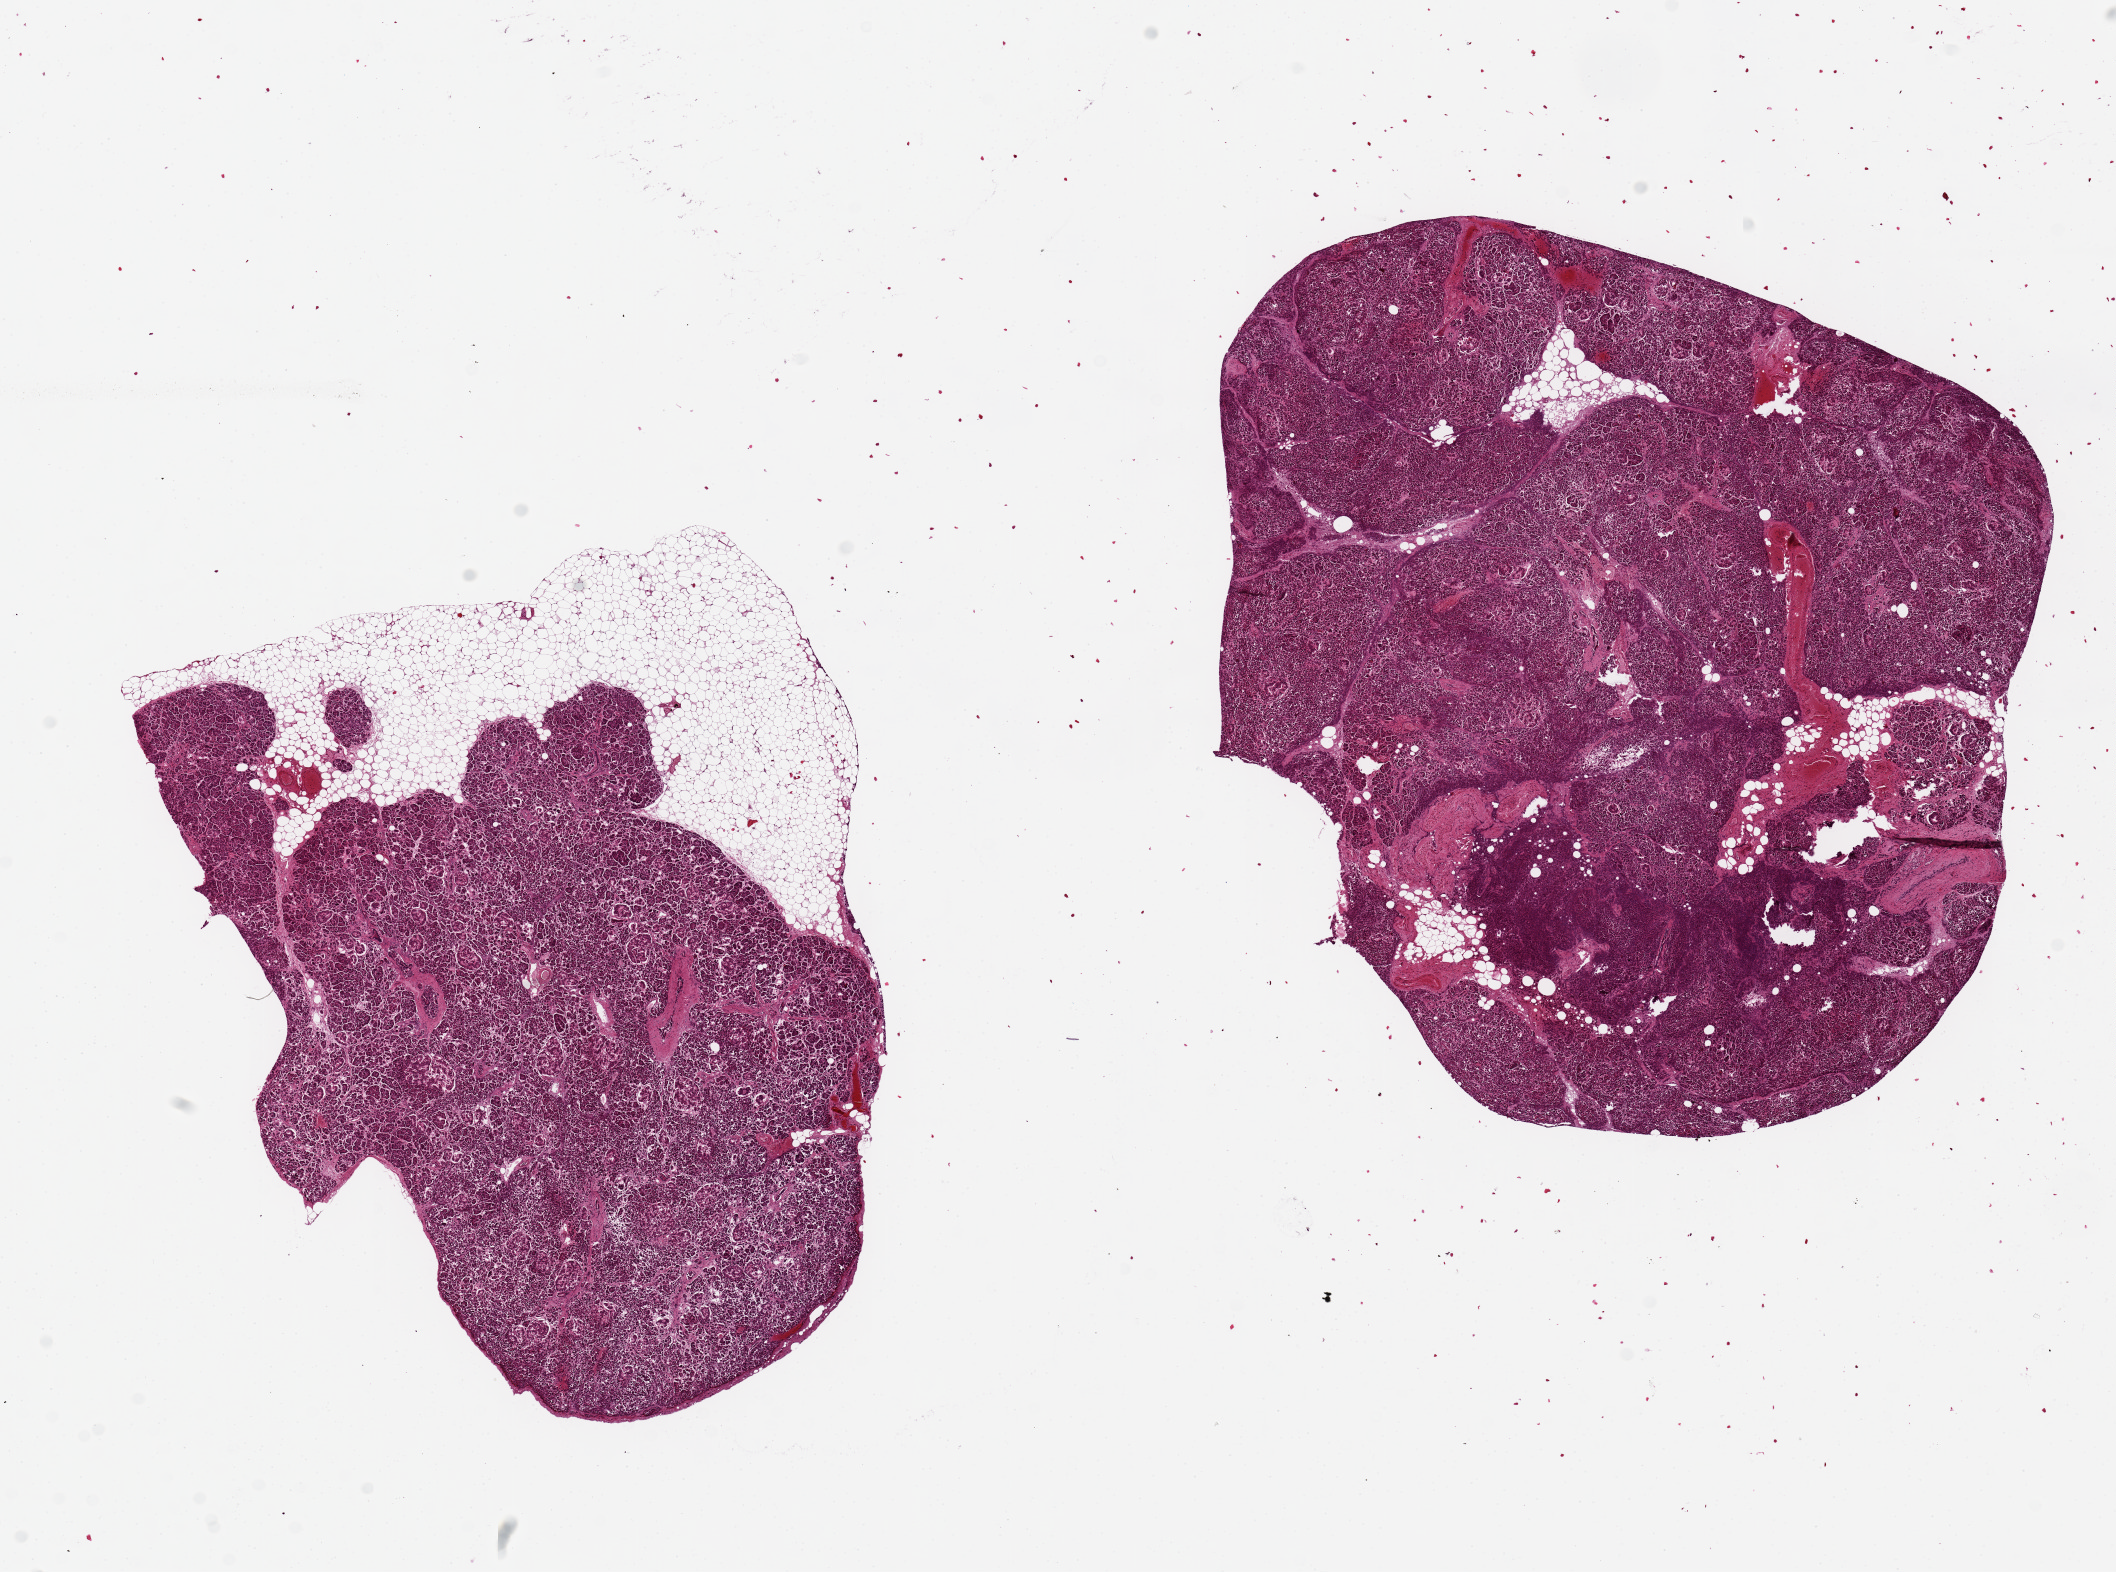
Digitized hematoxylin and eosin (H&E)-stained section, low-resolution overview of the scanned area, about 16.7 x 12.4 mm. Donor: male.
Specimen: PAXgene-fixed paraffin-embedded (PFPE) section; sampled site (target tissue): pancreas; donor tissue sample.